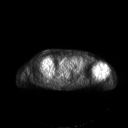
FDG PET of an extremity soft-tissue mass (from a PET/CT study), one axial slice. Position 150 of 267 along the scan axis. 3.27 mm slice thickness. 128 × 128 image matrix. Female patient, age 83 years. From the clinical record (not read from this slice): histological type: pleiomorphic leiomyosarcoma; grade: high; site of the primary tumour: left biceps.
Outlined on this slice (expert contour drawn on MRI and transferred to this co-registered scan by the dataset authors):
- gross tumour volume including surrounding oedema: bounding box <92,62,107,77> (left, top, right, bottom; pixels)
- gross tumour volume (mass): <92,62,107,77>